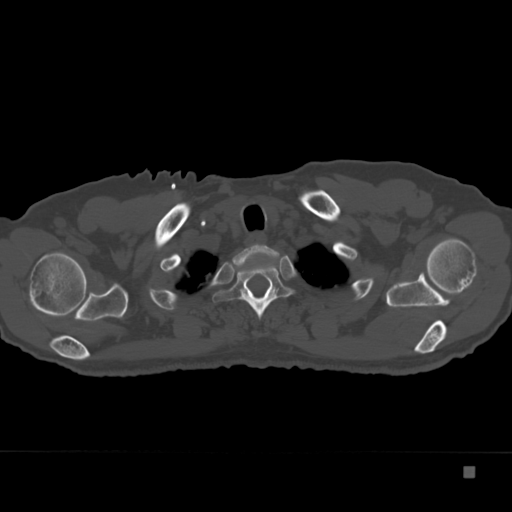
CT including the spine, one axial slice; position 304 of 332 along the scan axis; reconstruction kernel Br40s; 120 kVp; bone window (W 1800 / L 400 HU); 512 × 512 image matrix. Patient: male, 72 years. Case-level facts recorded for this patient, not image findings: primary cancer: skeletal.
Outlined on this slice (semi-automatic segmentation, software-assisted and operator-edited):
- T1 vertebra: bounding box <232,244,279,301> (left, top, right, bottom; pixels)
- T2 vertebra: <212,252,294,319>
- T3 vertebra: <266,288,269,293>